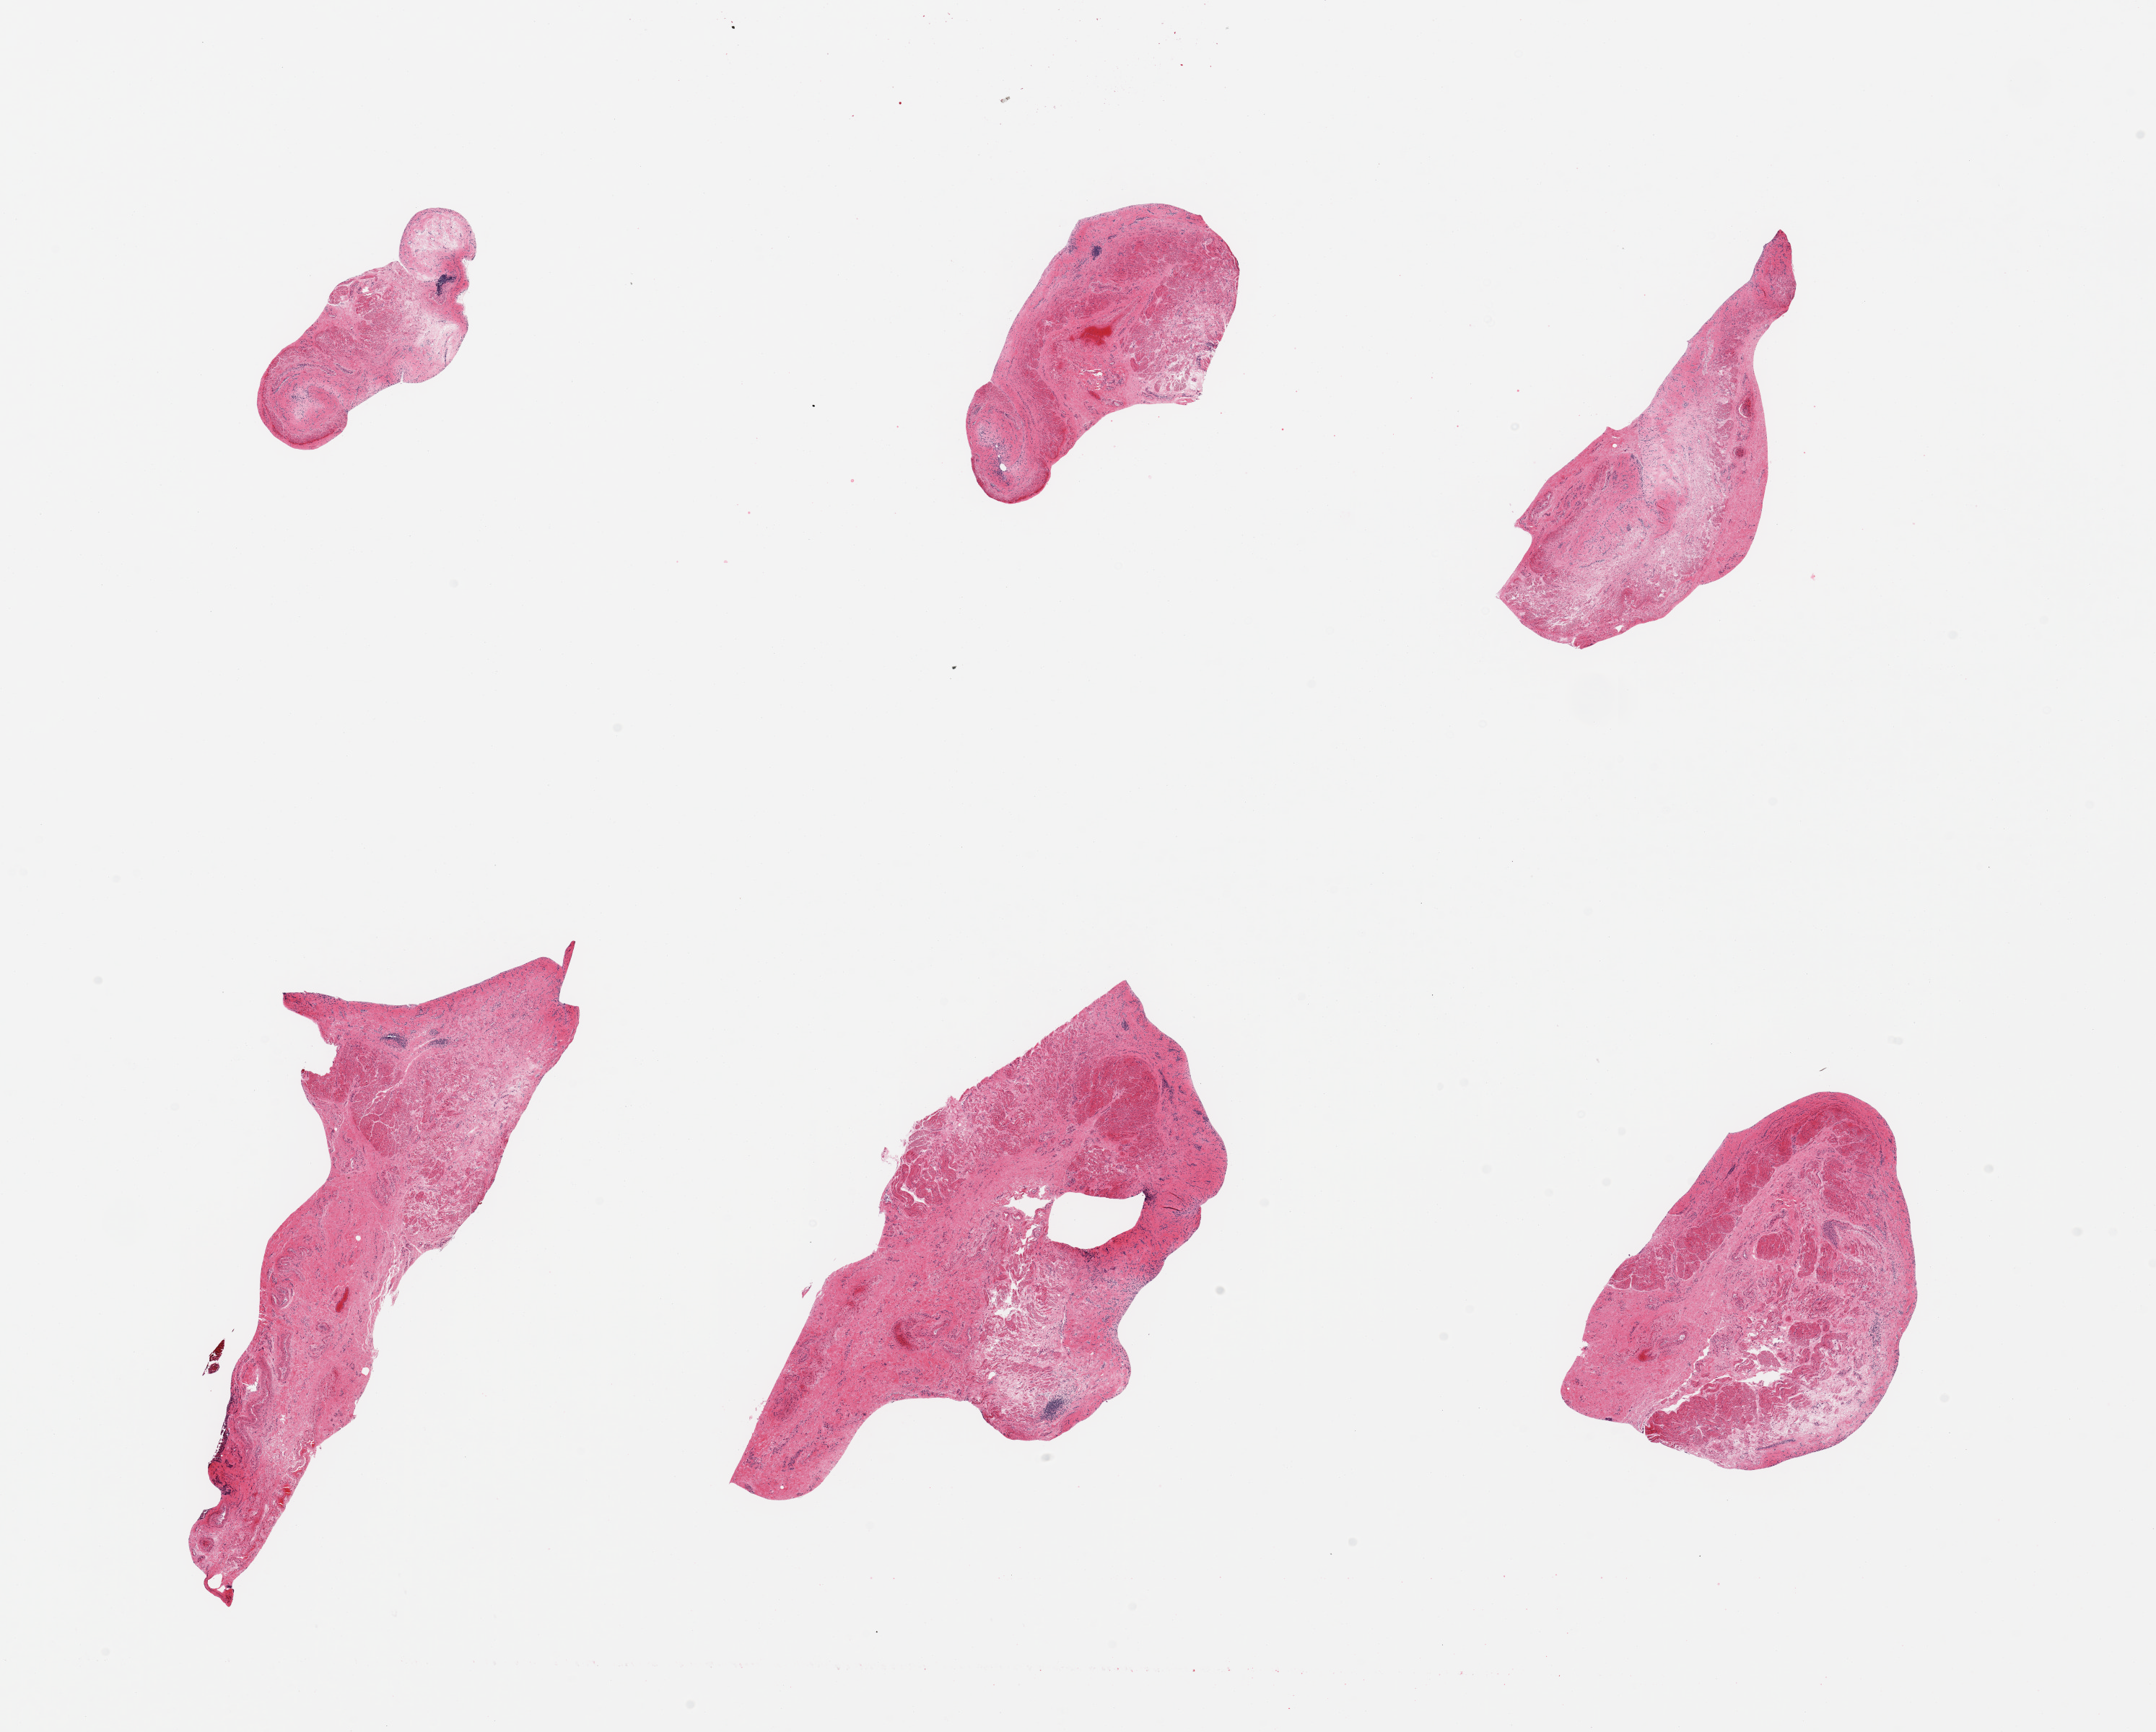
Hematoxylin and eosin (H&E) whole-slide image — low-resolution overview of the scanned area, about 23.6 x 19.0 mm, PAXgene-fixed paraffin-embedded (PFPE) section, sampled site (target tissue): esophageal mucous membrane, donor tissue sample. Donor sex: male.
Reviewer comment on this tissue sample: 6 pieces; submucosa, muscularis mucosae vs propria, no significant intact epithelium.